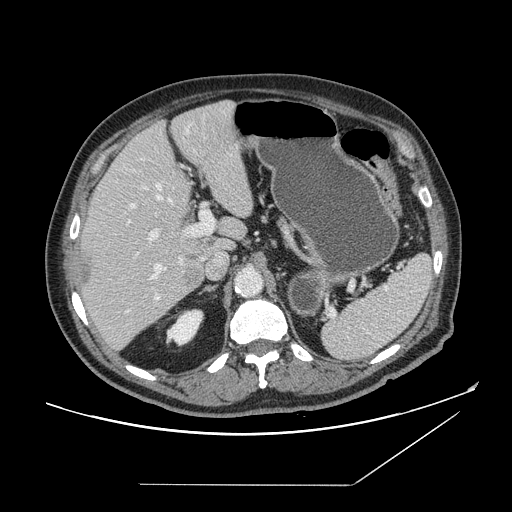
Contrast-enhanced abdominal CT, one axial slice; slice 102 of 166 in the series (ordered by position); 120 kVp; intravenous contrast given; soft-tissue window (W 400 / L 40 HU); 512 × 512 image matrix, field of view 416 × 416 mm. Male patient, age 80 years. From the clinical record (not read from this slice): diagnosis: colorectal cancer liver metastases, imaged before liver resection; multiple liver metastases: no; largest metastasis: 2.2 cm.
Annotated regions visible in this slice (manually delineated by an expert):
- hepatic veins: bounding box (x1, y1, x2, y2) in pixels: (127, 184, 172, 313)
- liver: (80, 102, 254, 350)
- planned liver remnant (the part of the liver to remain after resection): (89, 99, 254, 256)
- portal vein (with intrahepatic branches): (130, 203, 215, 300)
- liver metastasis: (83, 262, 192, 286)
- liver metastasis: (187, 280, 194, 286)